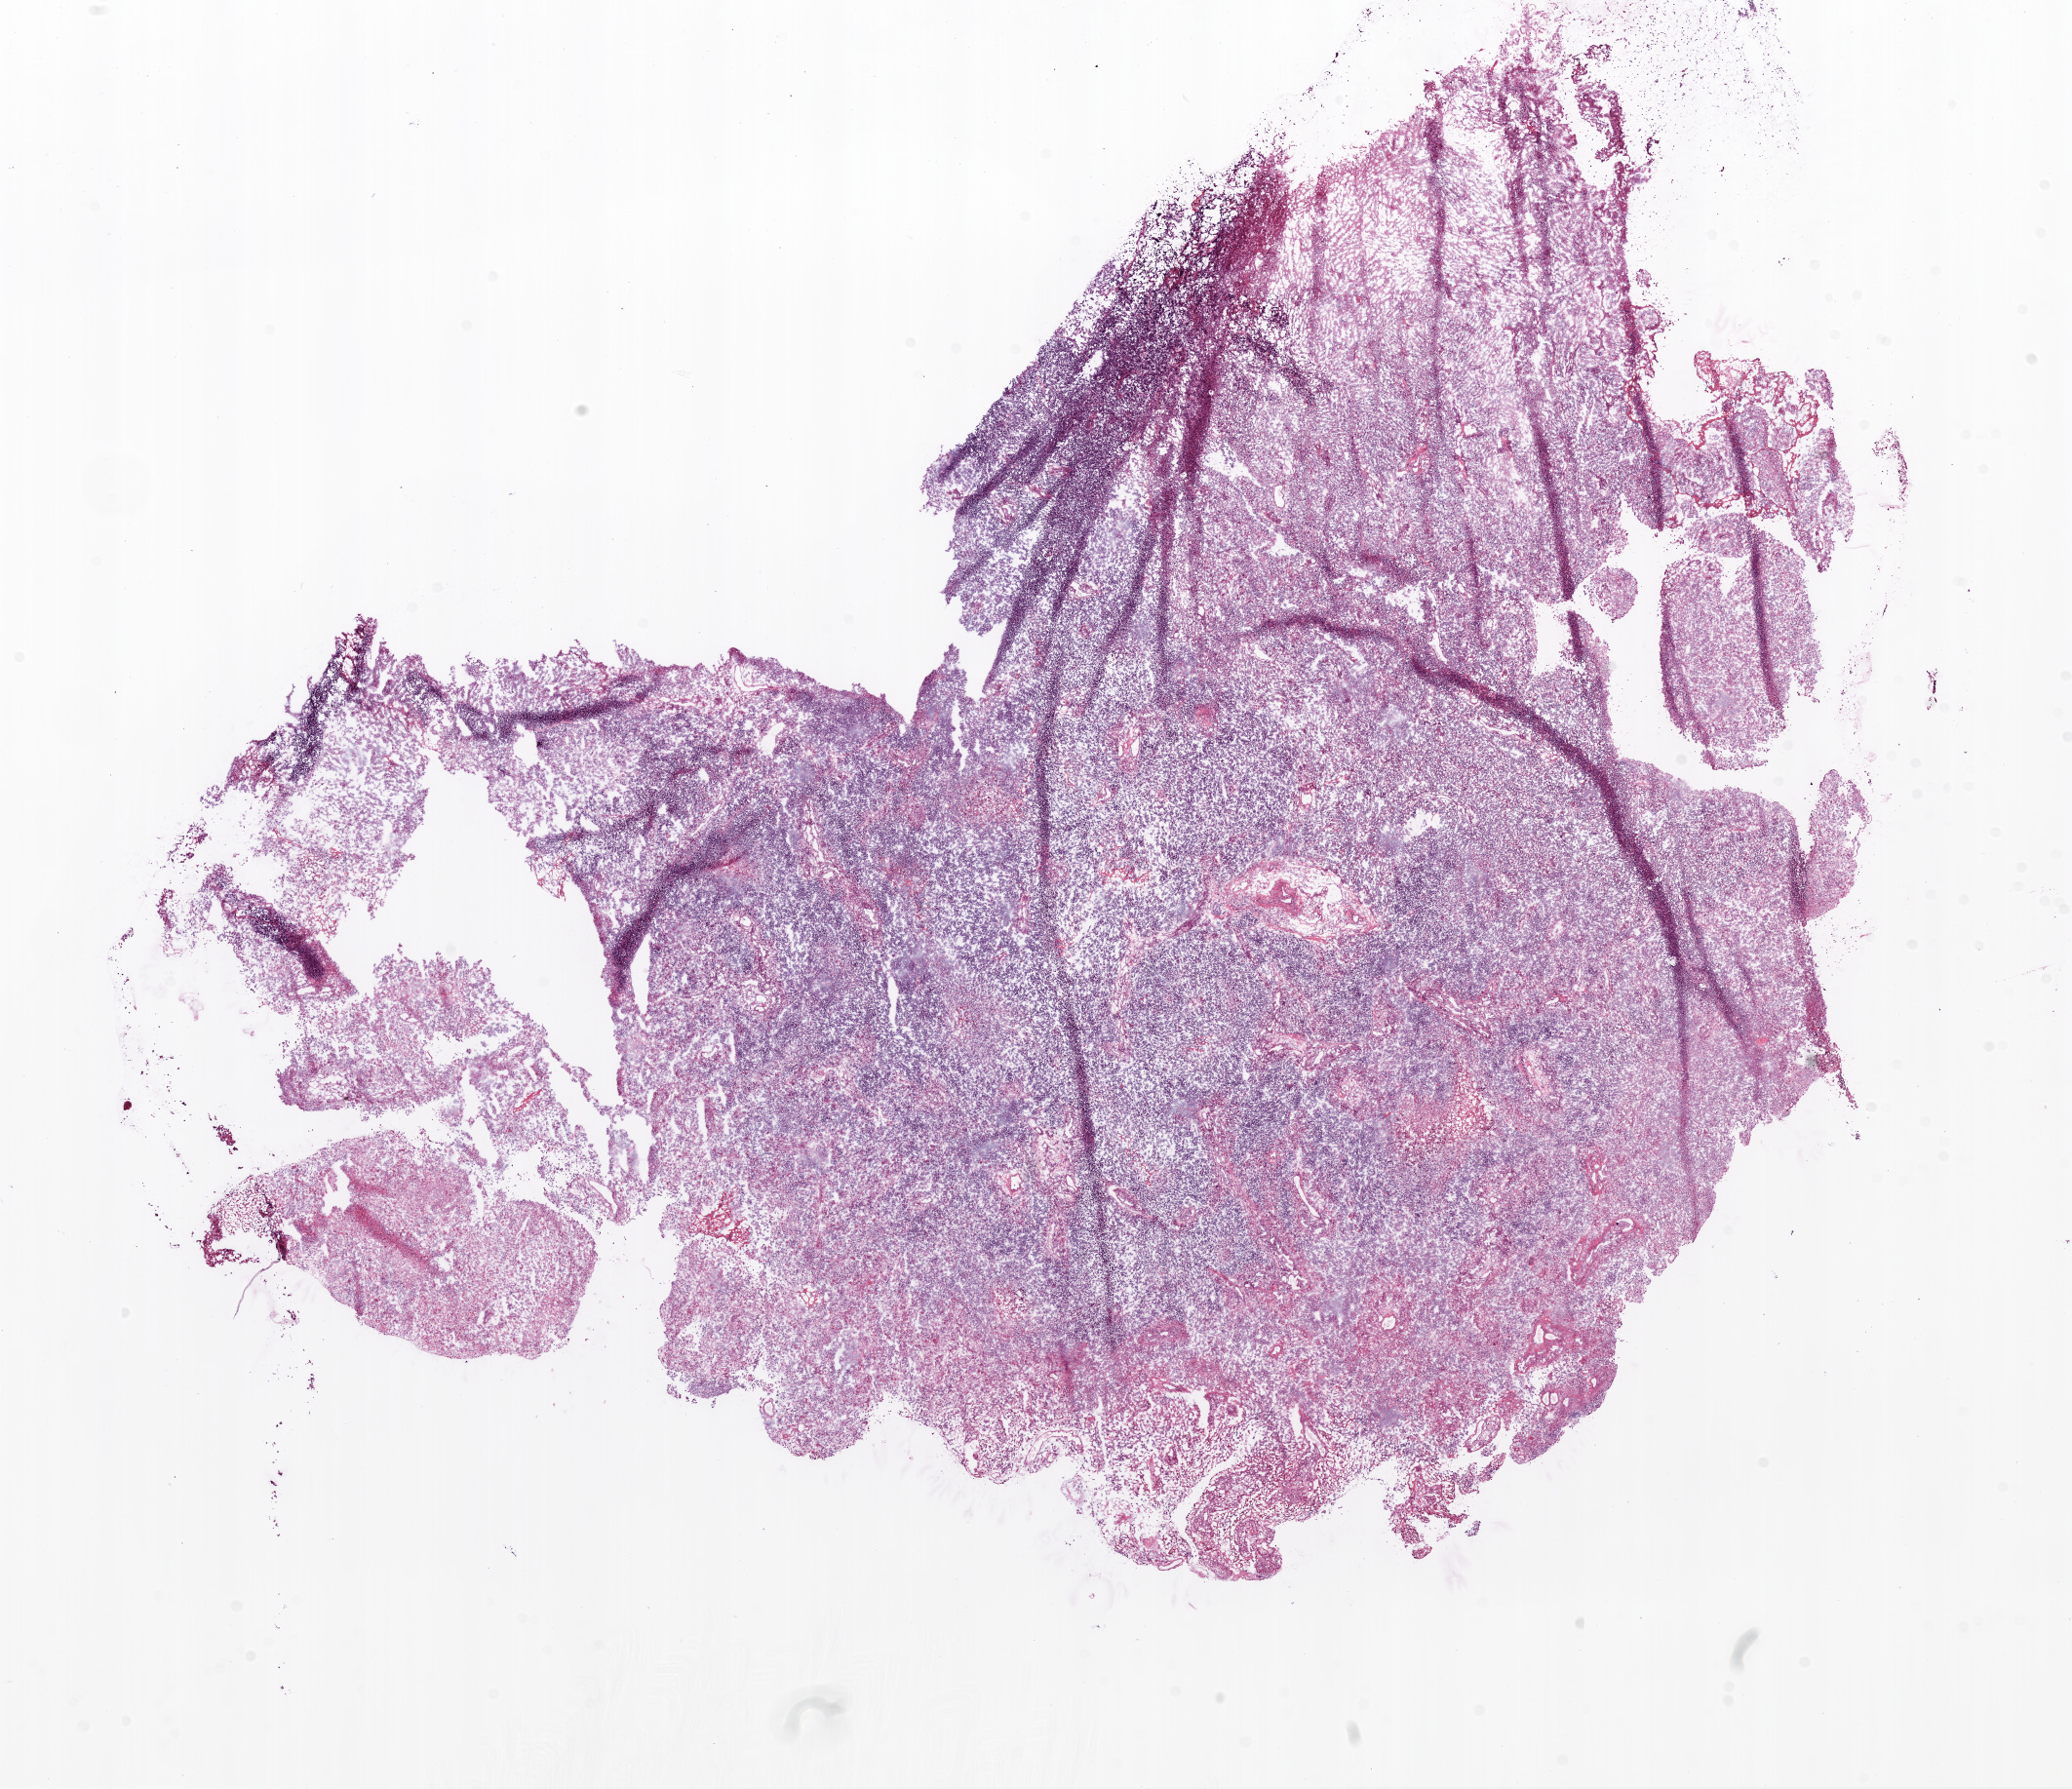
H&E-stained whole-slide image, a low-resolution overview of the entire scanned area, about 17.1 x 14.7 mm (acquisition: 20x scan). Frozen section from the top of the tissue portion. Primary tumour sample from the brain. Male, age 61 years at initial diagnosis. Slide review estimates, as recorded: tumour cells 95%, tumour nuclei 80%, normal cells 0%, stromal cells 0%, necrosis 5%.
* histologic diagnosis: Glioblastoma